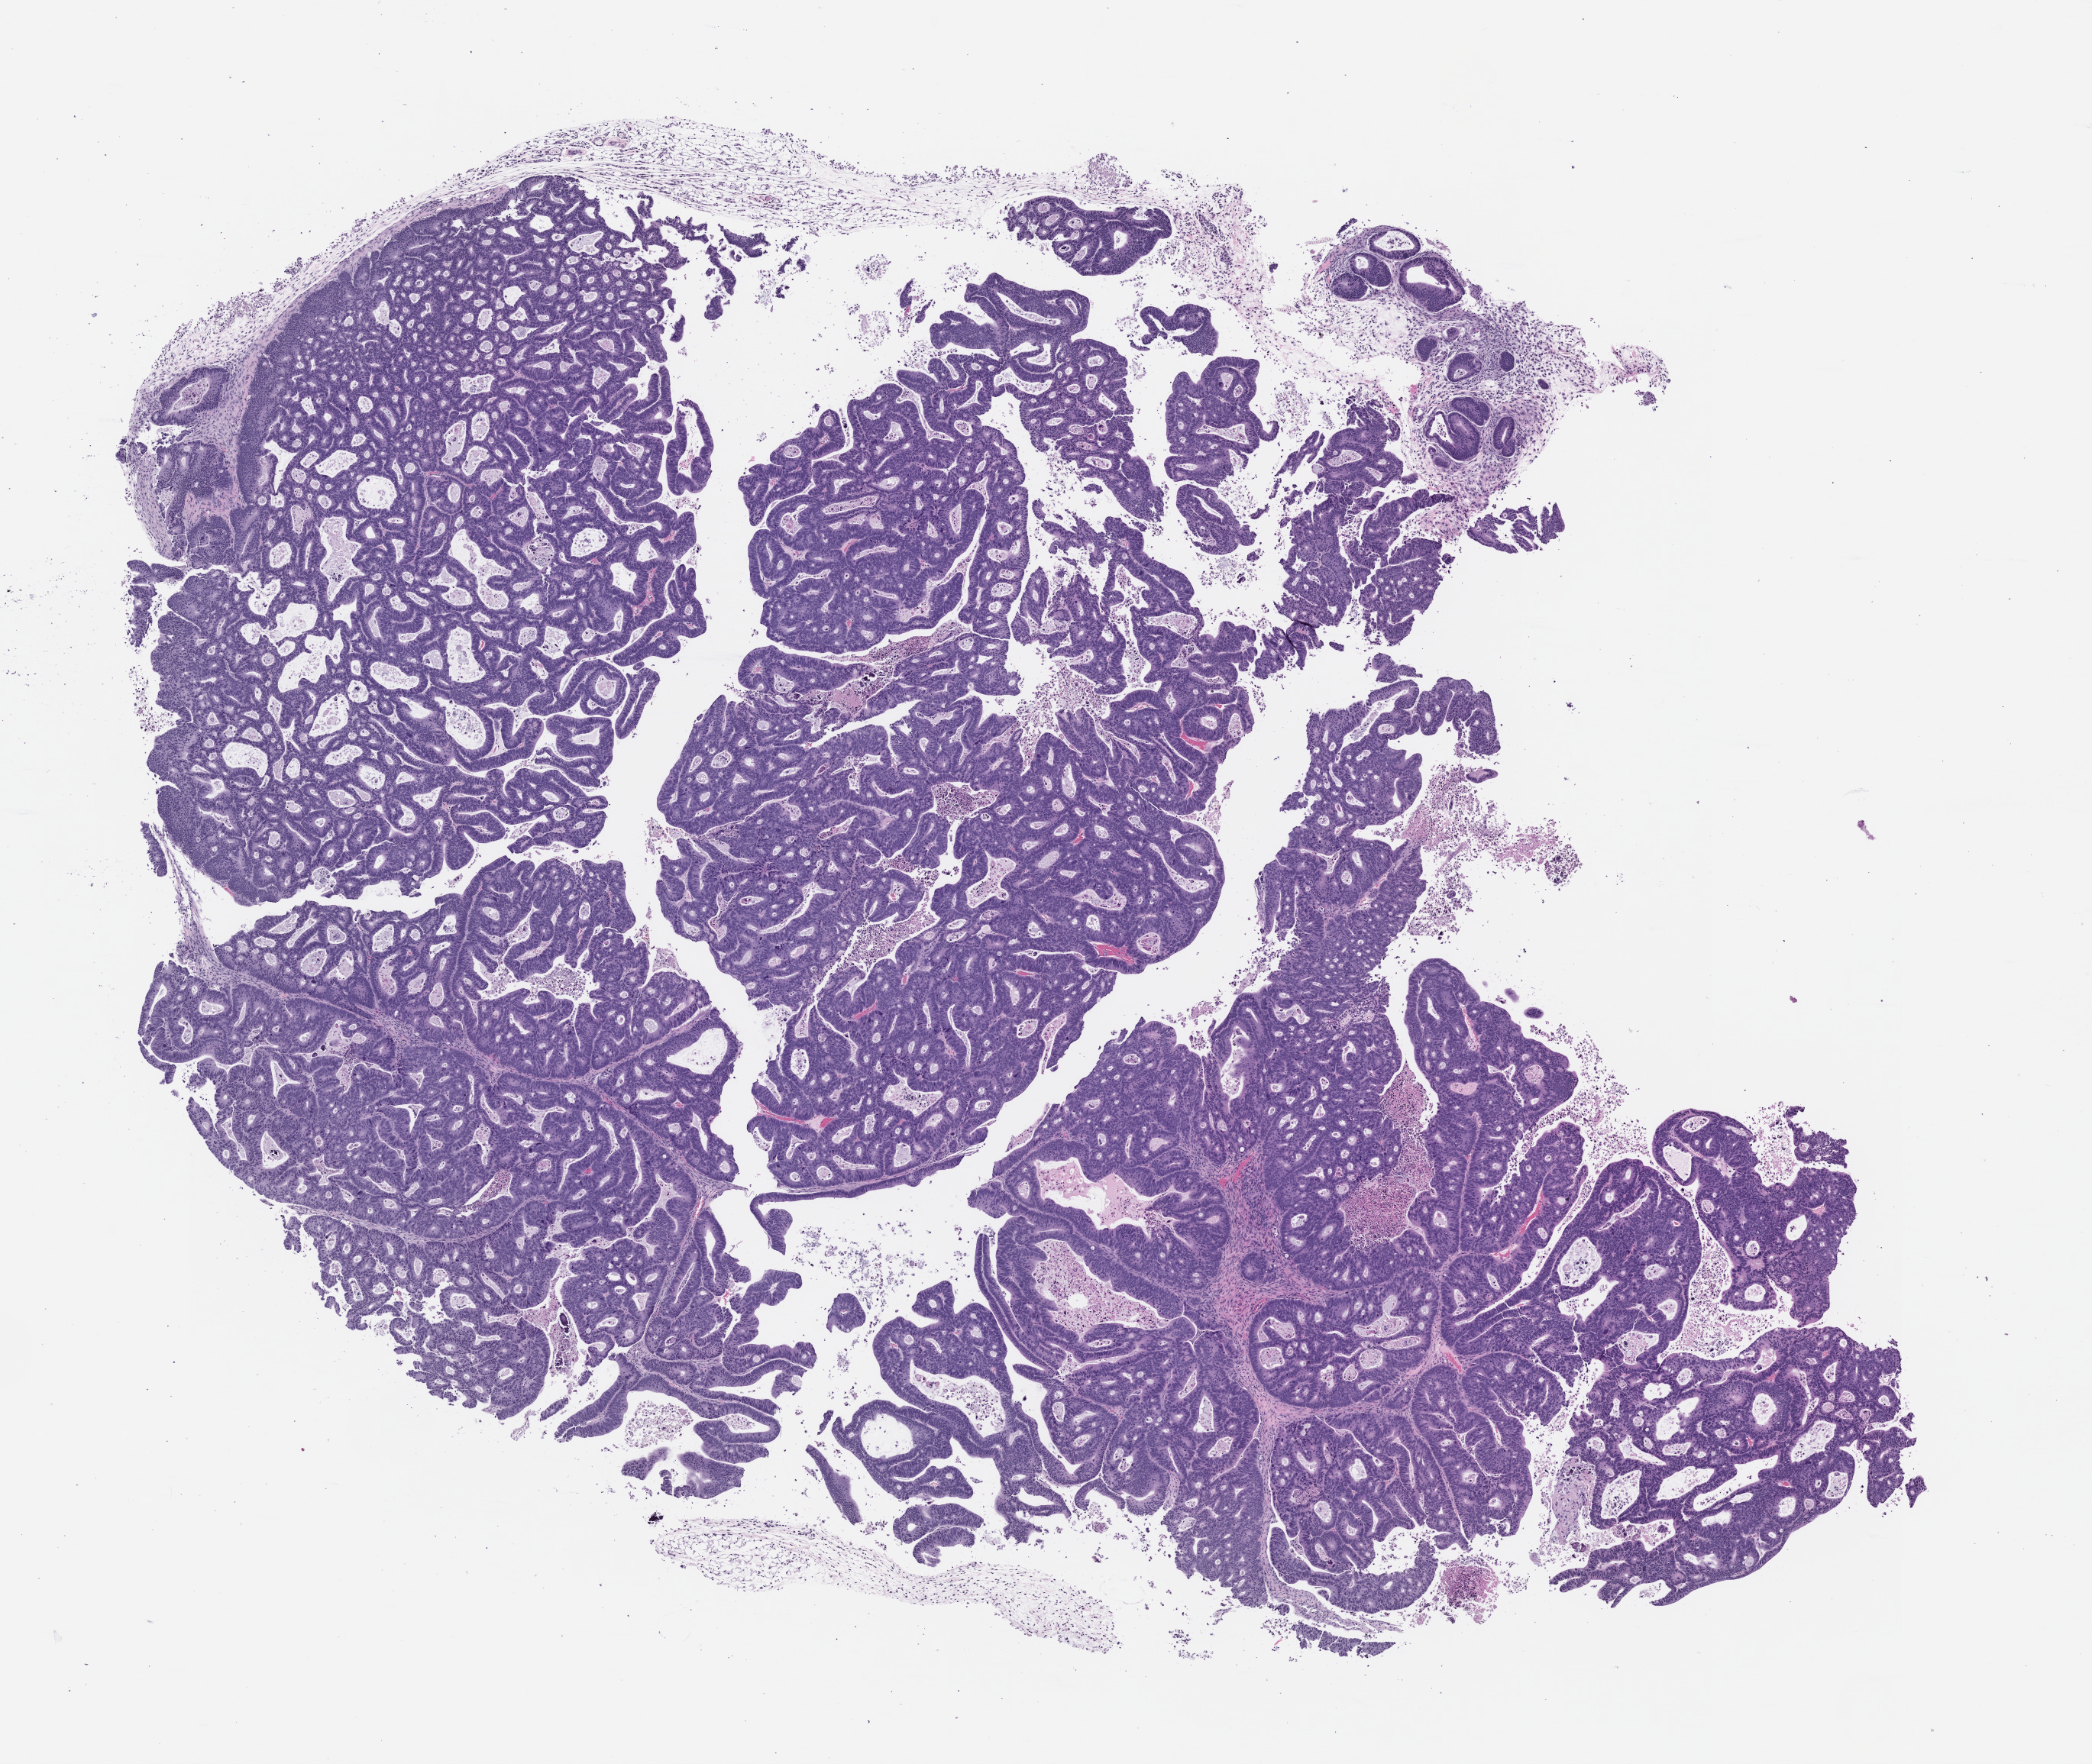
Whole-slide image, haematoxylin and eosin: patient-derived xenograft (human tumor grown in a mouse), passage 1 — whole scanned area (about 11.0 x 9.3 mm) shown as a low-resolution overview; formalin-fixed, paraffin-embedded (FFPE) tissue; originating tumor site category: colon.
• originating patient diagnosis: Colon Adenocarcinoma